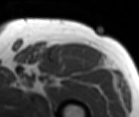
MRI of an extremity soft-tissue mass, one axial slice; slice 76 of 86 in the series (ordered by position); MR volume resampled by the dataset authors to the PET/CT grid (not the native acquisition matrix); 139 × 117 image matrix, field of view 136 × 114 mm. Male patient. From the clinical record (not read from this slice): histological type: extraskeletal osteosarcoma; grade: high; site of the primary tumour: thigh.
Outlined on this slice (expert contour drawn on MRI and transferred to this co-registered scan by the dataset authors):
- gross tumour volume (mass): bounding box <54,43,103,67> (left, top, right, bottom; pixels)